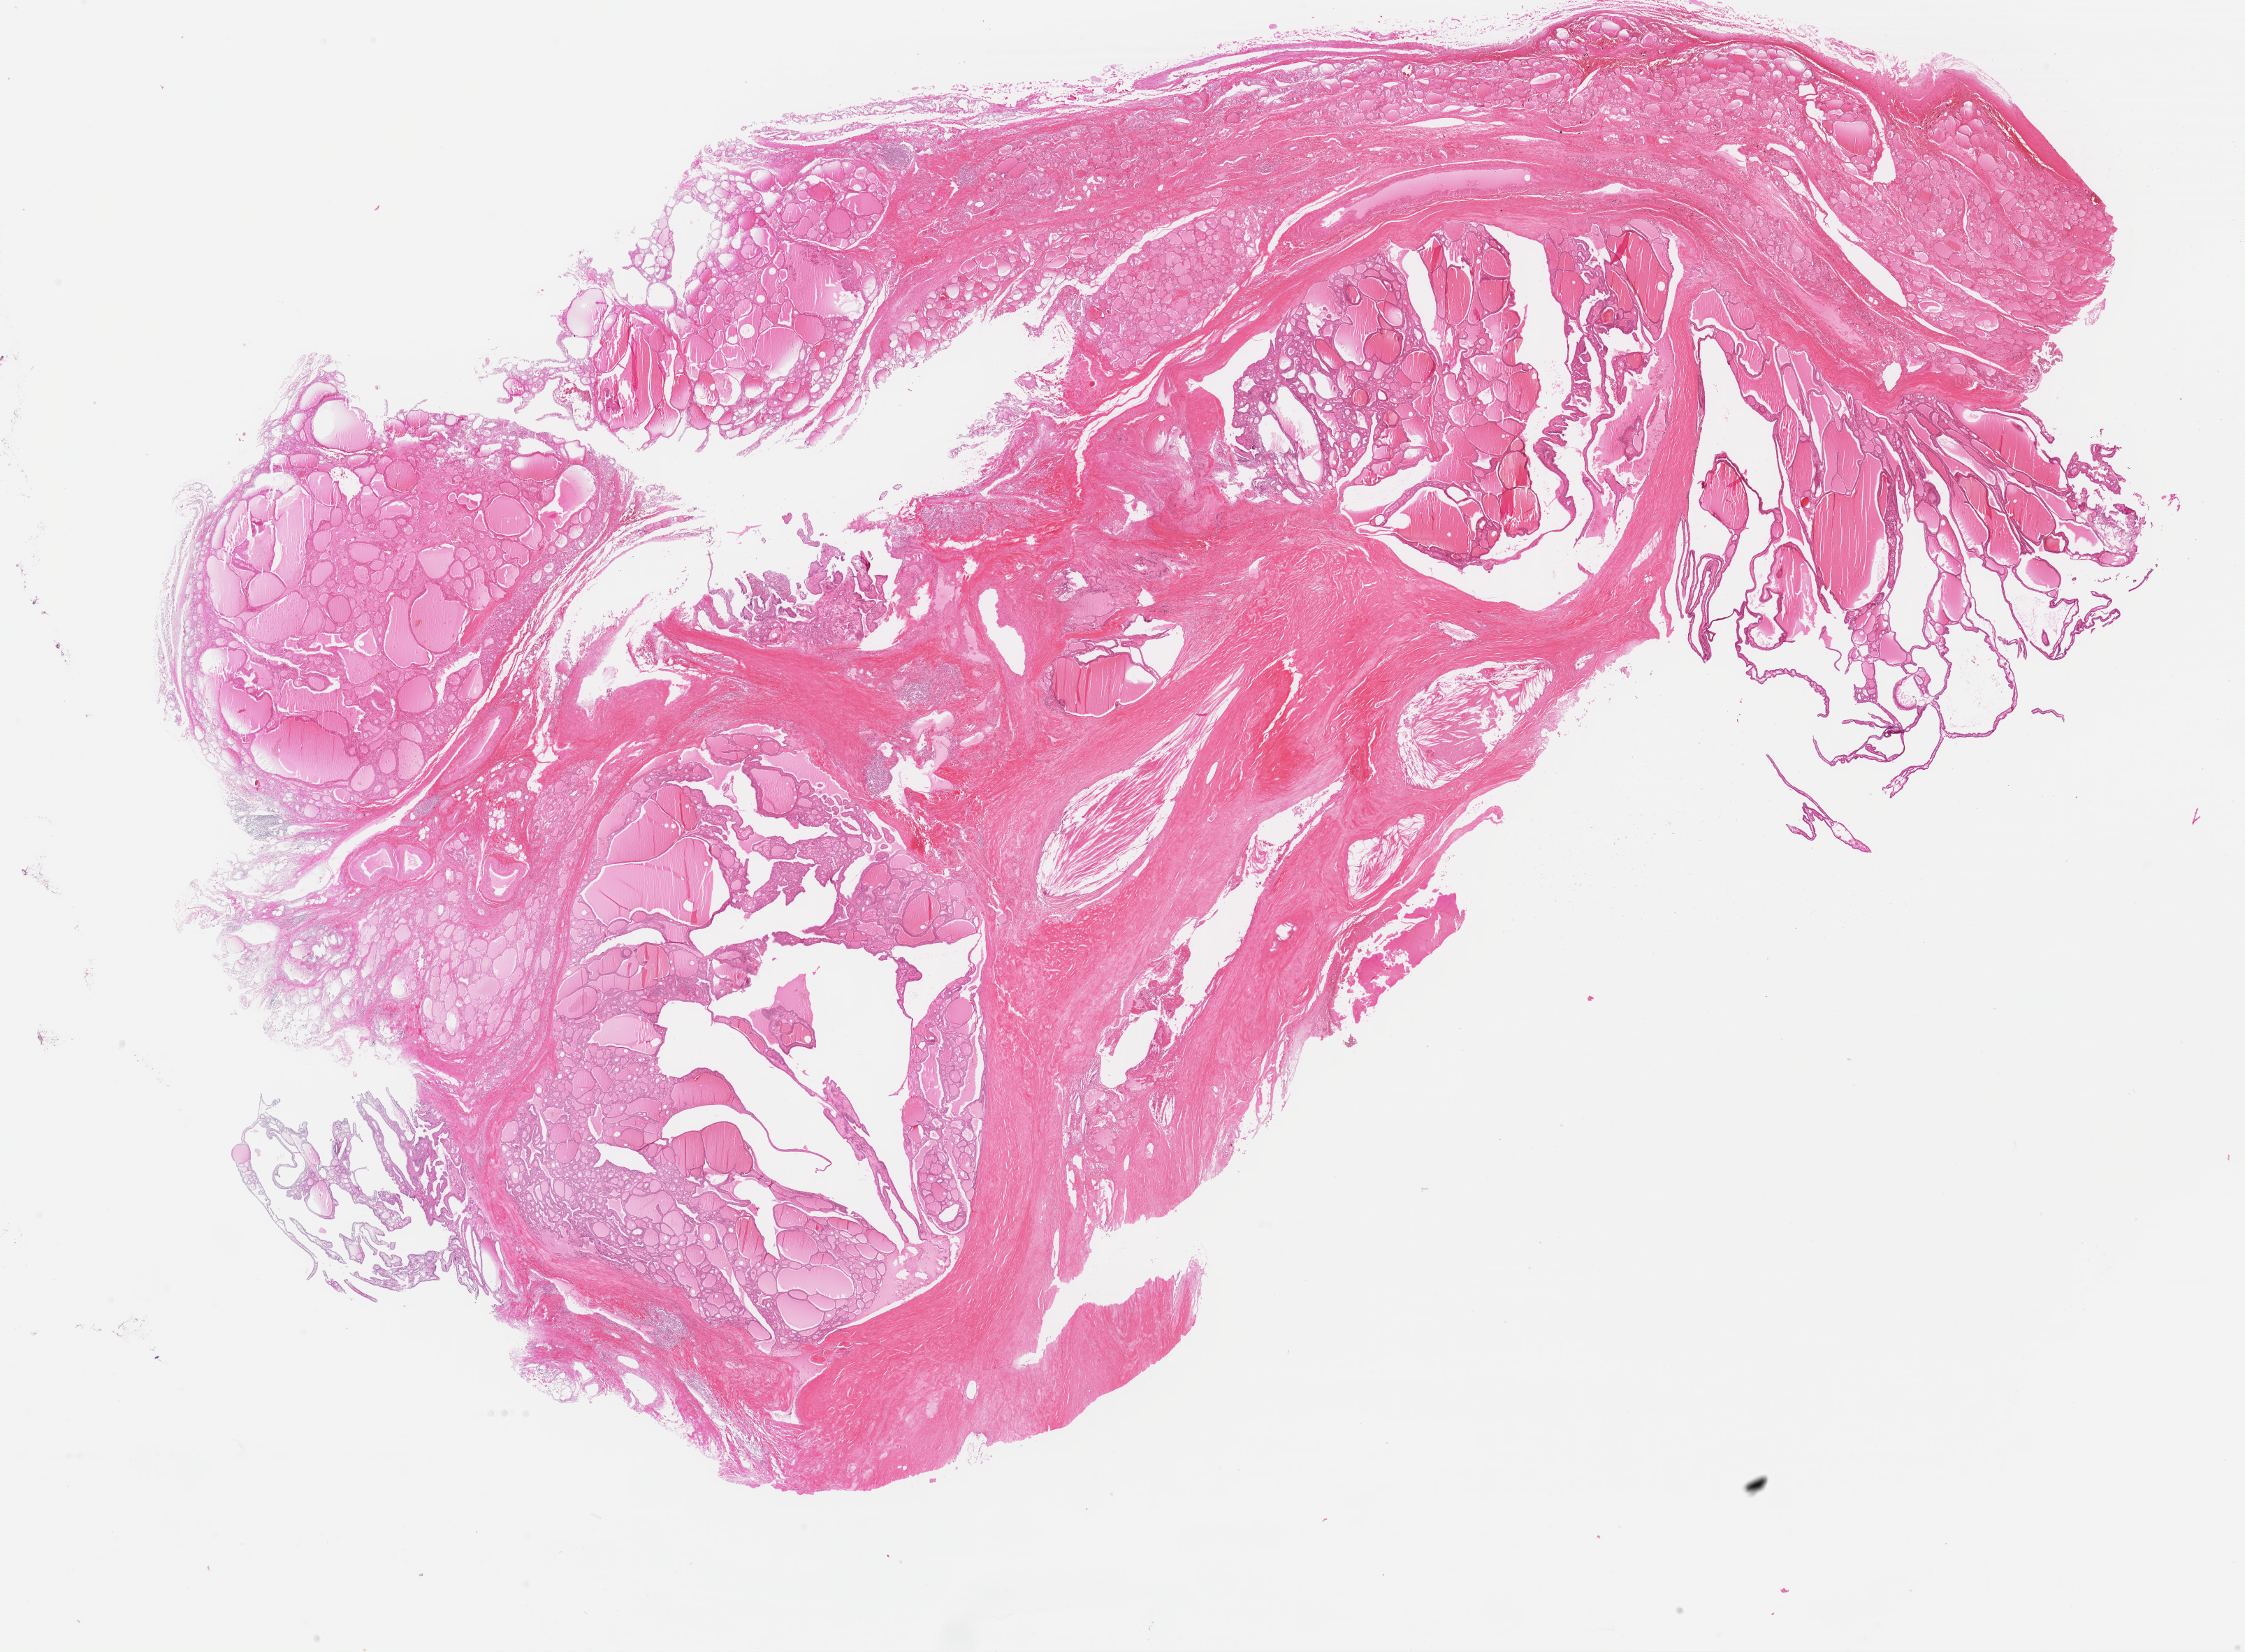
H&E-stained whole-slide image, whole scanned area (about 25.4 x 18.7 mm) shown as a low-resolution overview. Formalin-fixed paraffin-embedded (FFPE) diagnostic section. Primary tumour sample from the thyroid. Male patient.
Pathologic diagnosis: Papillary adenocarcinoma, NOS. Laterality: bilateral. Lymph nodes positive (case pathology): 10 of 41 examined. AJCC pathologic stage: III (5th edition).